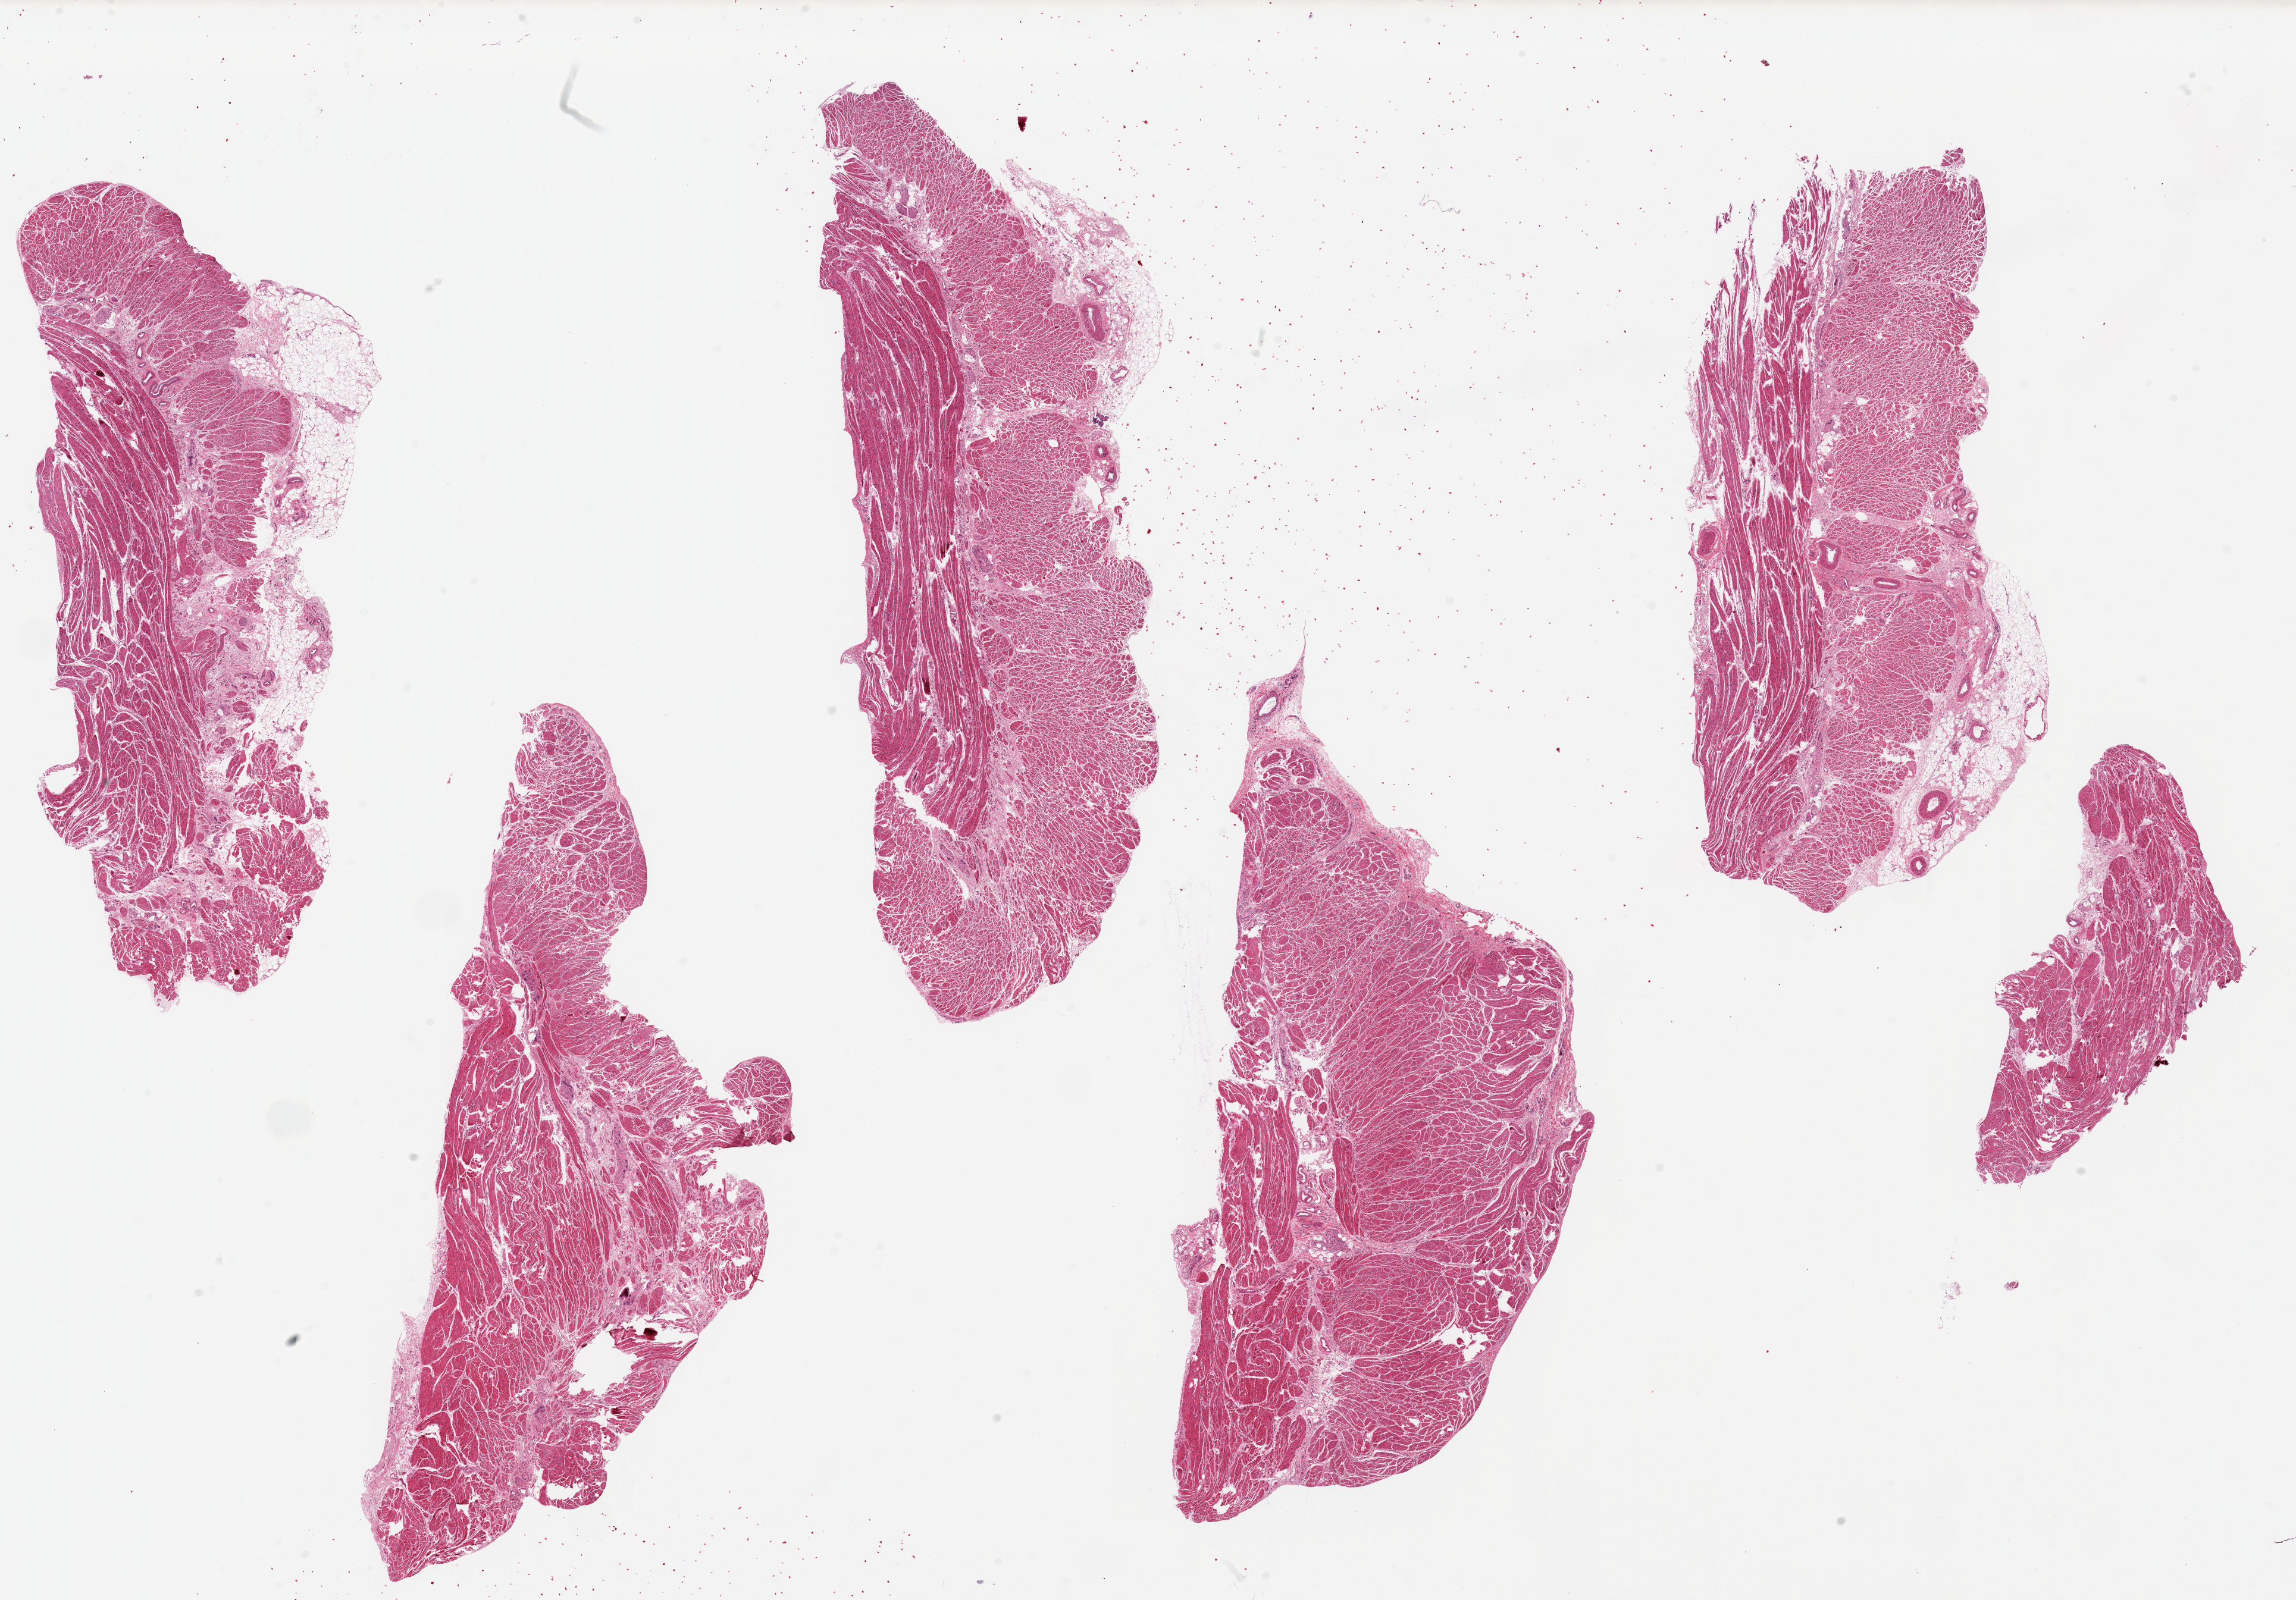
Hematoxylin and eosin (H&E) whole-slide image — low-resolution overview of the scanned area, about 30.5 x 21.3 mm (from a 20x scan). PAXgene-fixed paraffin-embedded (PFPE) section. Target tissue: gastroesophageal junction. Donor tissue sample. Donor: male.
Reviewer comment on this tissue sample: 6 pieces, up to 12x5mm; Up to 1x3mm adipose on 2 pieces.